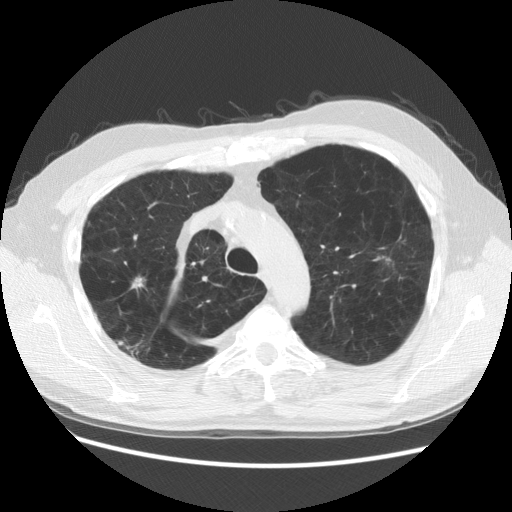
Low-dose screening chest CT, one axial slice. Slice 104 of 137 in the series (ordered by position). Reconstruction kernel STANDARD. 140 kVp. Lung window (W 1500 / L -600 HU). 512 × 512 image matrix, field of view 377 × 377 mm.
Structures marked on this image (manually delineated by an expert):
- lesion 1 (tumor, upper lobe of right lung): bounding box [x1, y1, x2, y2] px = [131, 276, 146, 289]